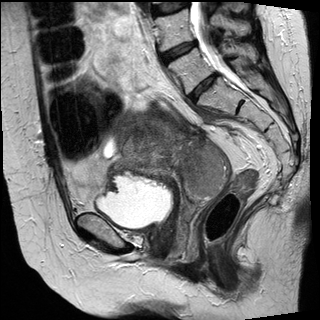
Pelvic MRI for cervical cancer, one sagittal slice. Position 14 of 30 along the scan axis. T2-weighted. 1.5 T. TE 89 ms, TR 3810 ms. 4 mm slice thickness. 320 × 320 image matrix. Female patient, age 62 years.
Outlined on this slice (outlined manually by an expert reader):
- uterus and cervix: bounding box [x1, y1, x2, y2] px = [118, 113, 233, 202]